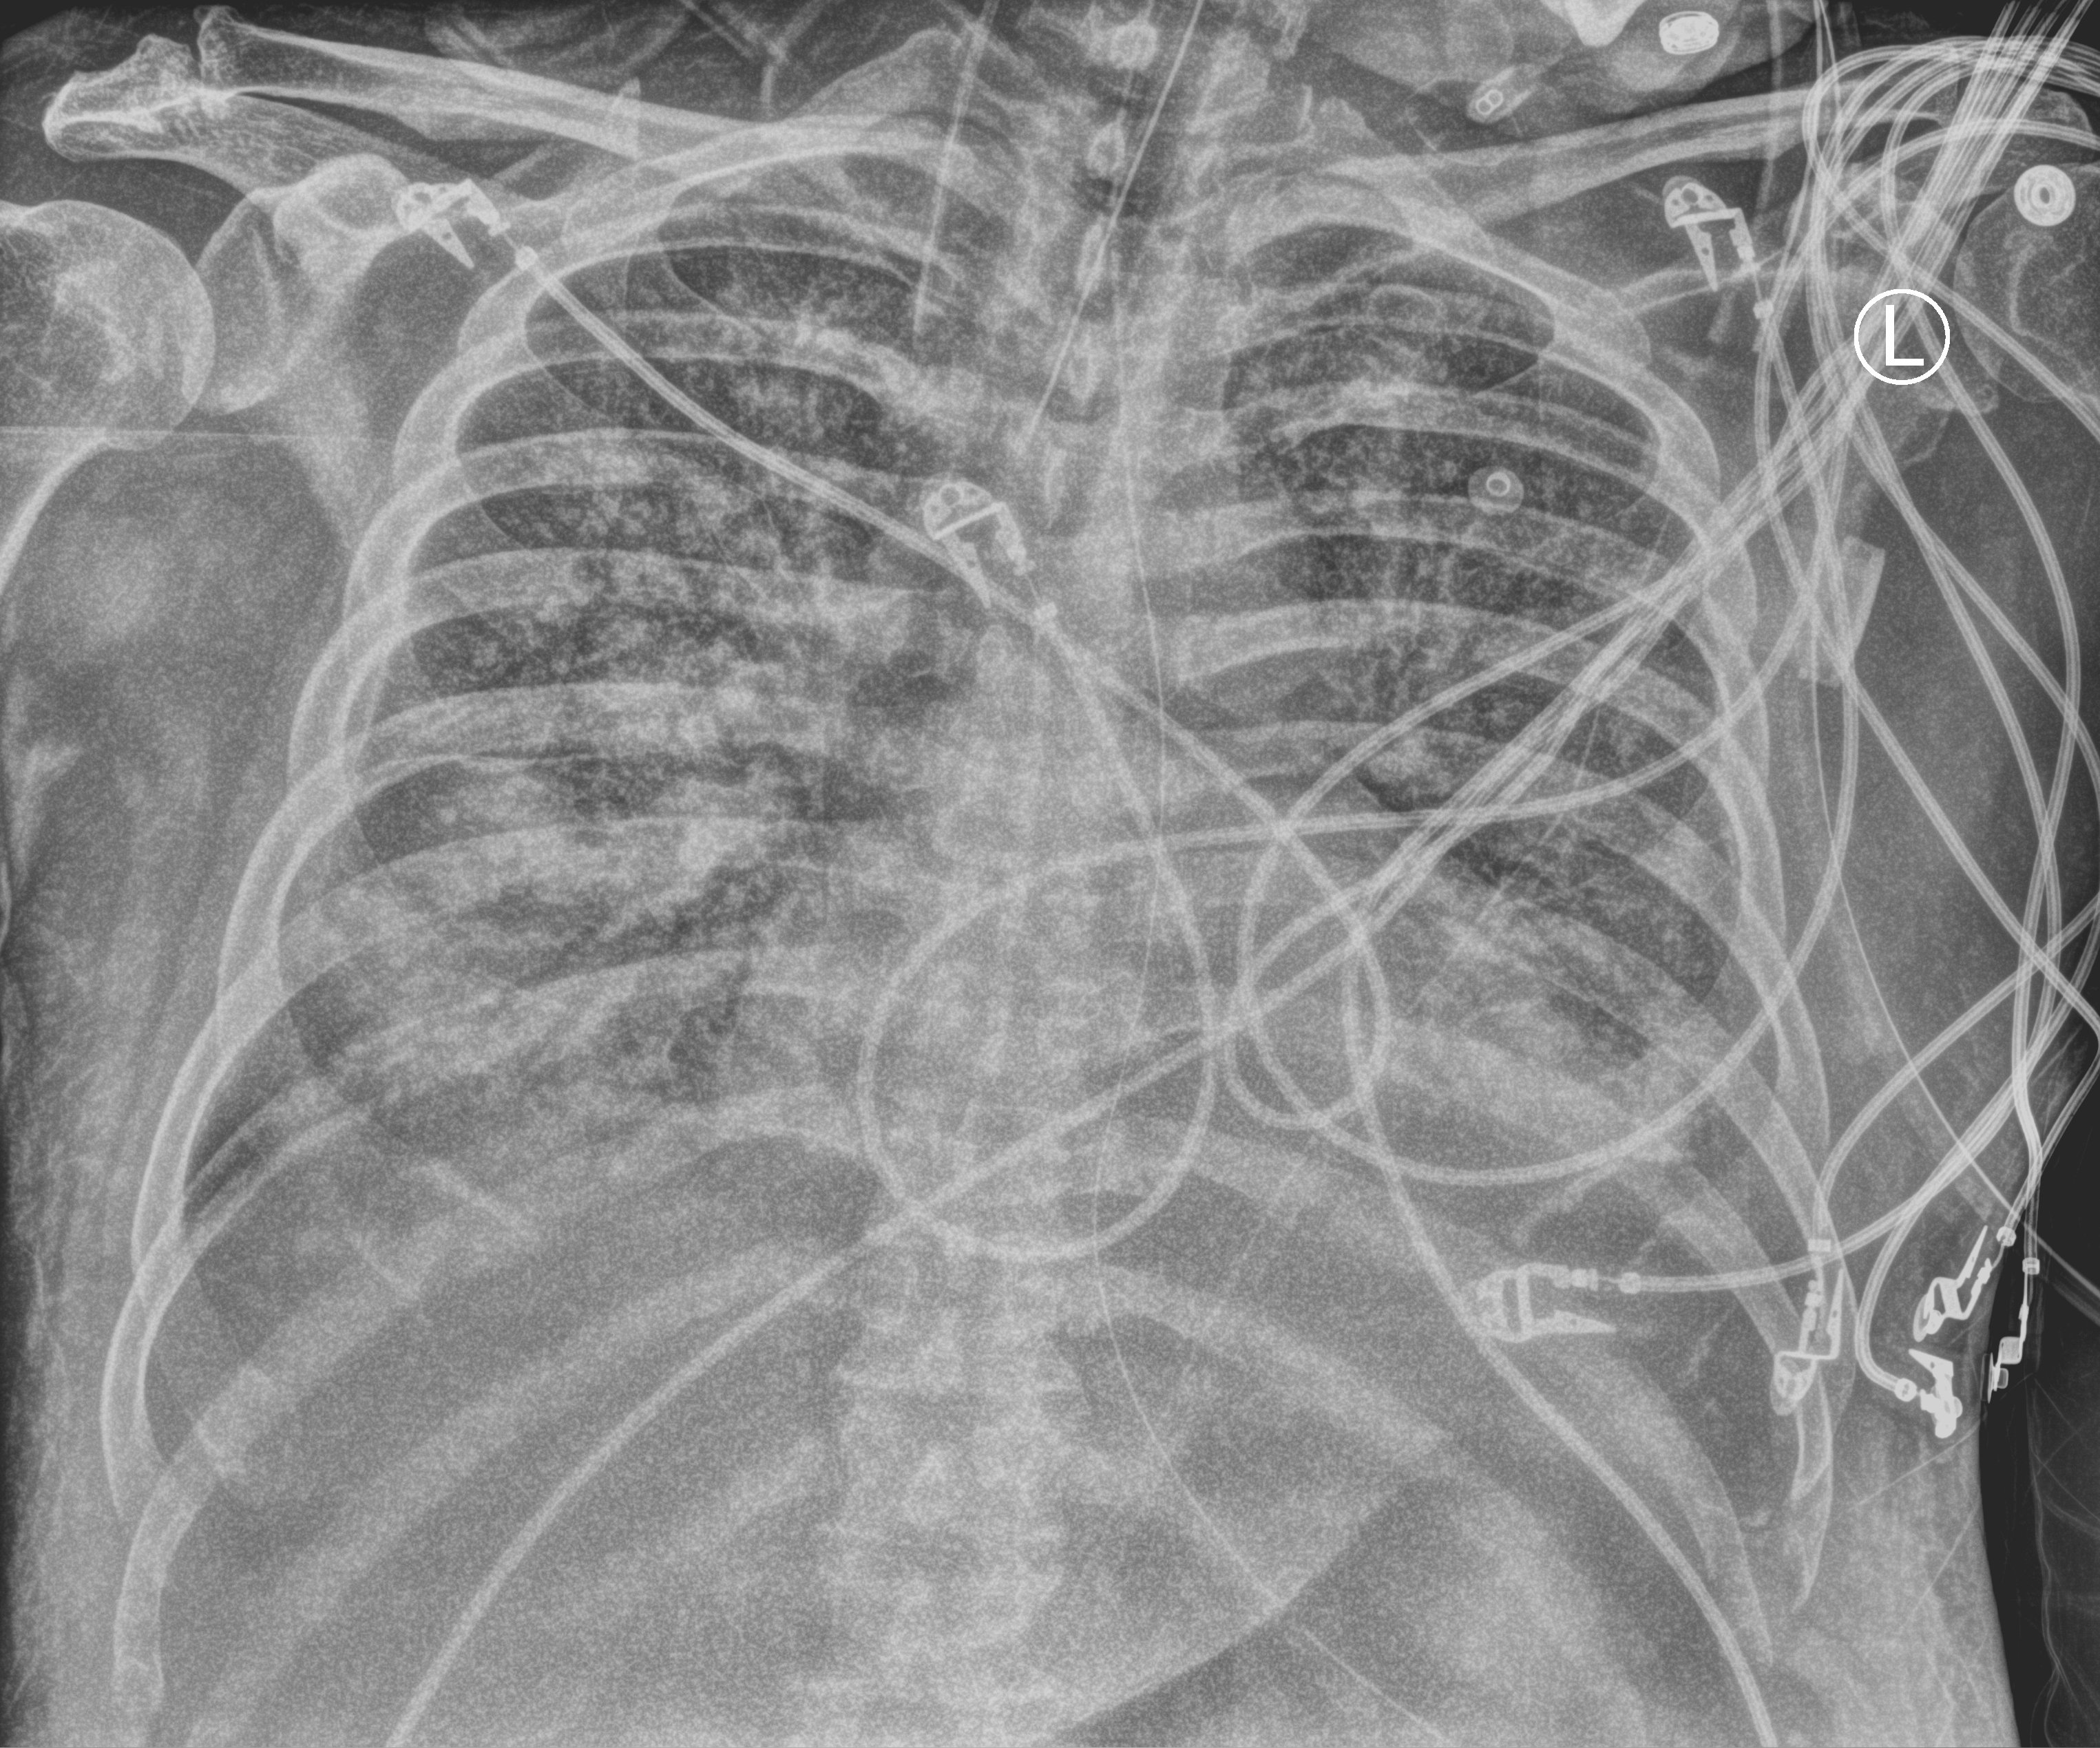
Chest X-ray (portable), anteroposterior (AP) projection. Male patient hospitalised with COVID-19, age 60–74 years.
From the hospital-stay record, not from the radiograph (when in the stay this image was taken is not recorded): COPD (admission record): no; length of hospital stay: 28 days; mechanically ventilated during this hospital stay: yes.